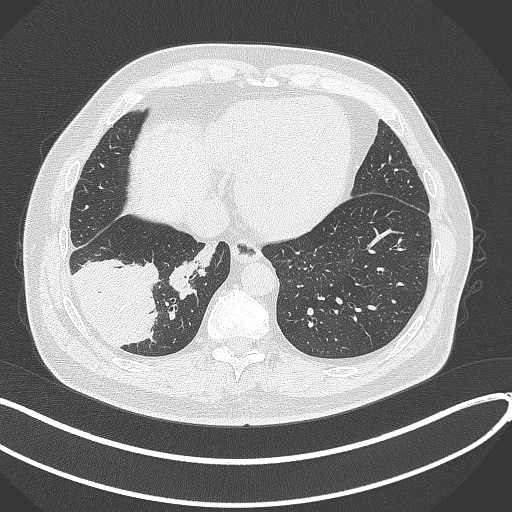
Chest CT, one axial slice; slice 92 of 360 in the series (ordered by position); 120 kVp; lung window (W 1500 / L -600 HU); 1 mm slice thickness; 512 × 512 image matrix, field of view 400 × 400 mm. Male patient, age 59 years.
Structures marked on this image (bounding box drawn by a radiologist):
- lung tumour (recorded histology: adenocarcinoma): box from (x=72, y=252) to (x=162, y=347) px